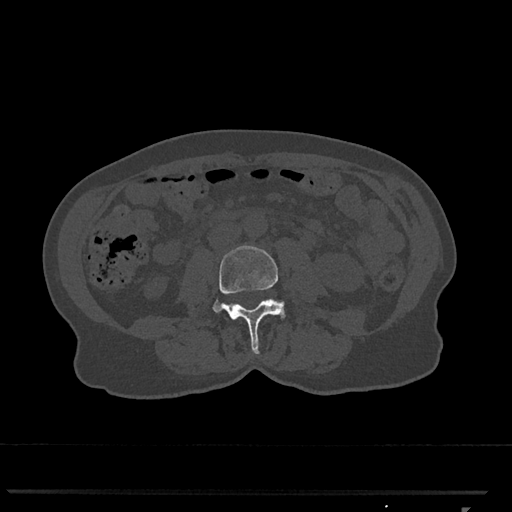
CT including the spine, one axial slice. Position 267 of 793 along the scan axis. Reconstruction kernel Br40s/3. 120 kVp. Bone window (W 1800 / L 400 HU). 512 × 512 image matrix, field of view 380 × 380 mm. Patient: female, 62 years. Case-level facts recorded for this patient, not image findings: primary cancer: renal.
Outlined on this slice (semi-automatically segmented with operator editing):
- L3 vertebra: bounding box <212,245,285,354> (left, top, right, bottom; pixels)